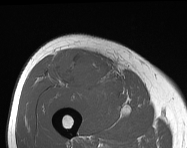
MRI of an extremity soft-tissue mass, one axial slice; position 70 of 114 along the scan axis; MR volume resampled by the dataset authors to the PET/CT grid (not the native acquisition matrix); 3.27 mm slice thickness; 187 × 148 image matrix, field of view 183 × 145 mm. Male patient. From the clinical record (not read from this slice): histological type: pleiomorphic leiomyosarcoma; grade: intermediate; site of the primary tumour: right thigh.
Outlined on this slice (expert contour drawn on MRI and transferred to this co-registered scan by the dataset authors):
- gross tumour volume including surrounding oedema: bounding box <57,50,112,89> (left, top, right, bottom; pixels)
- gross tumour volume (mass): <63,56,108,87>